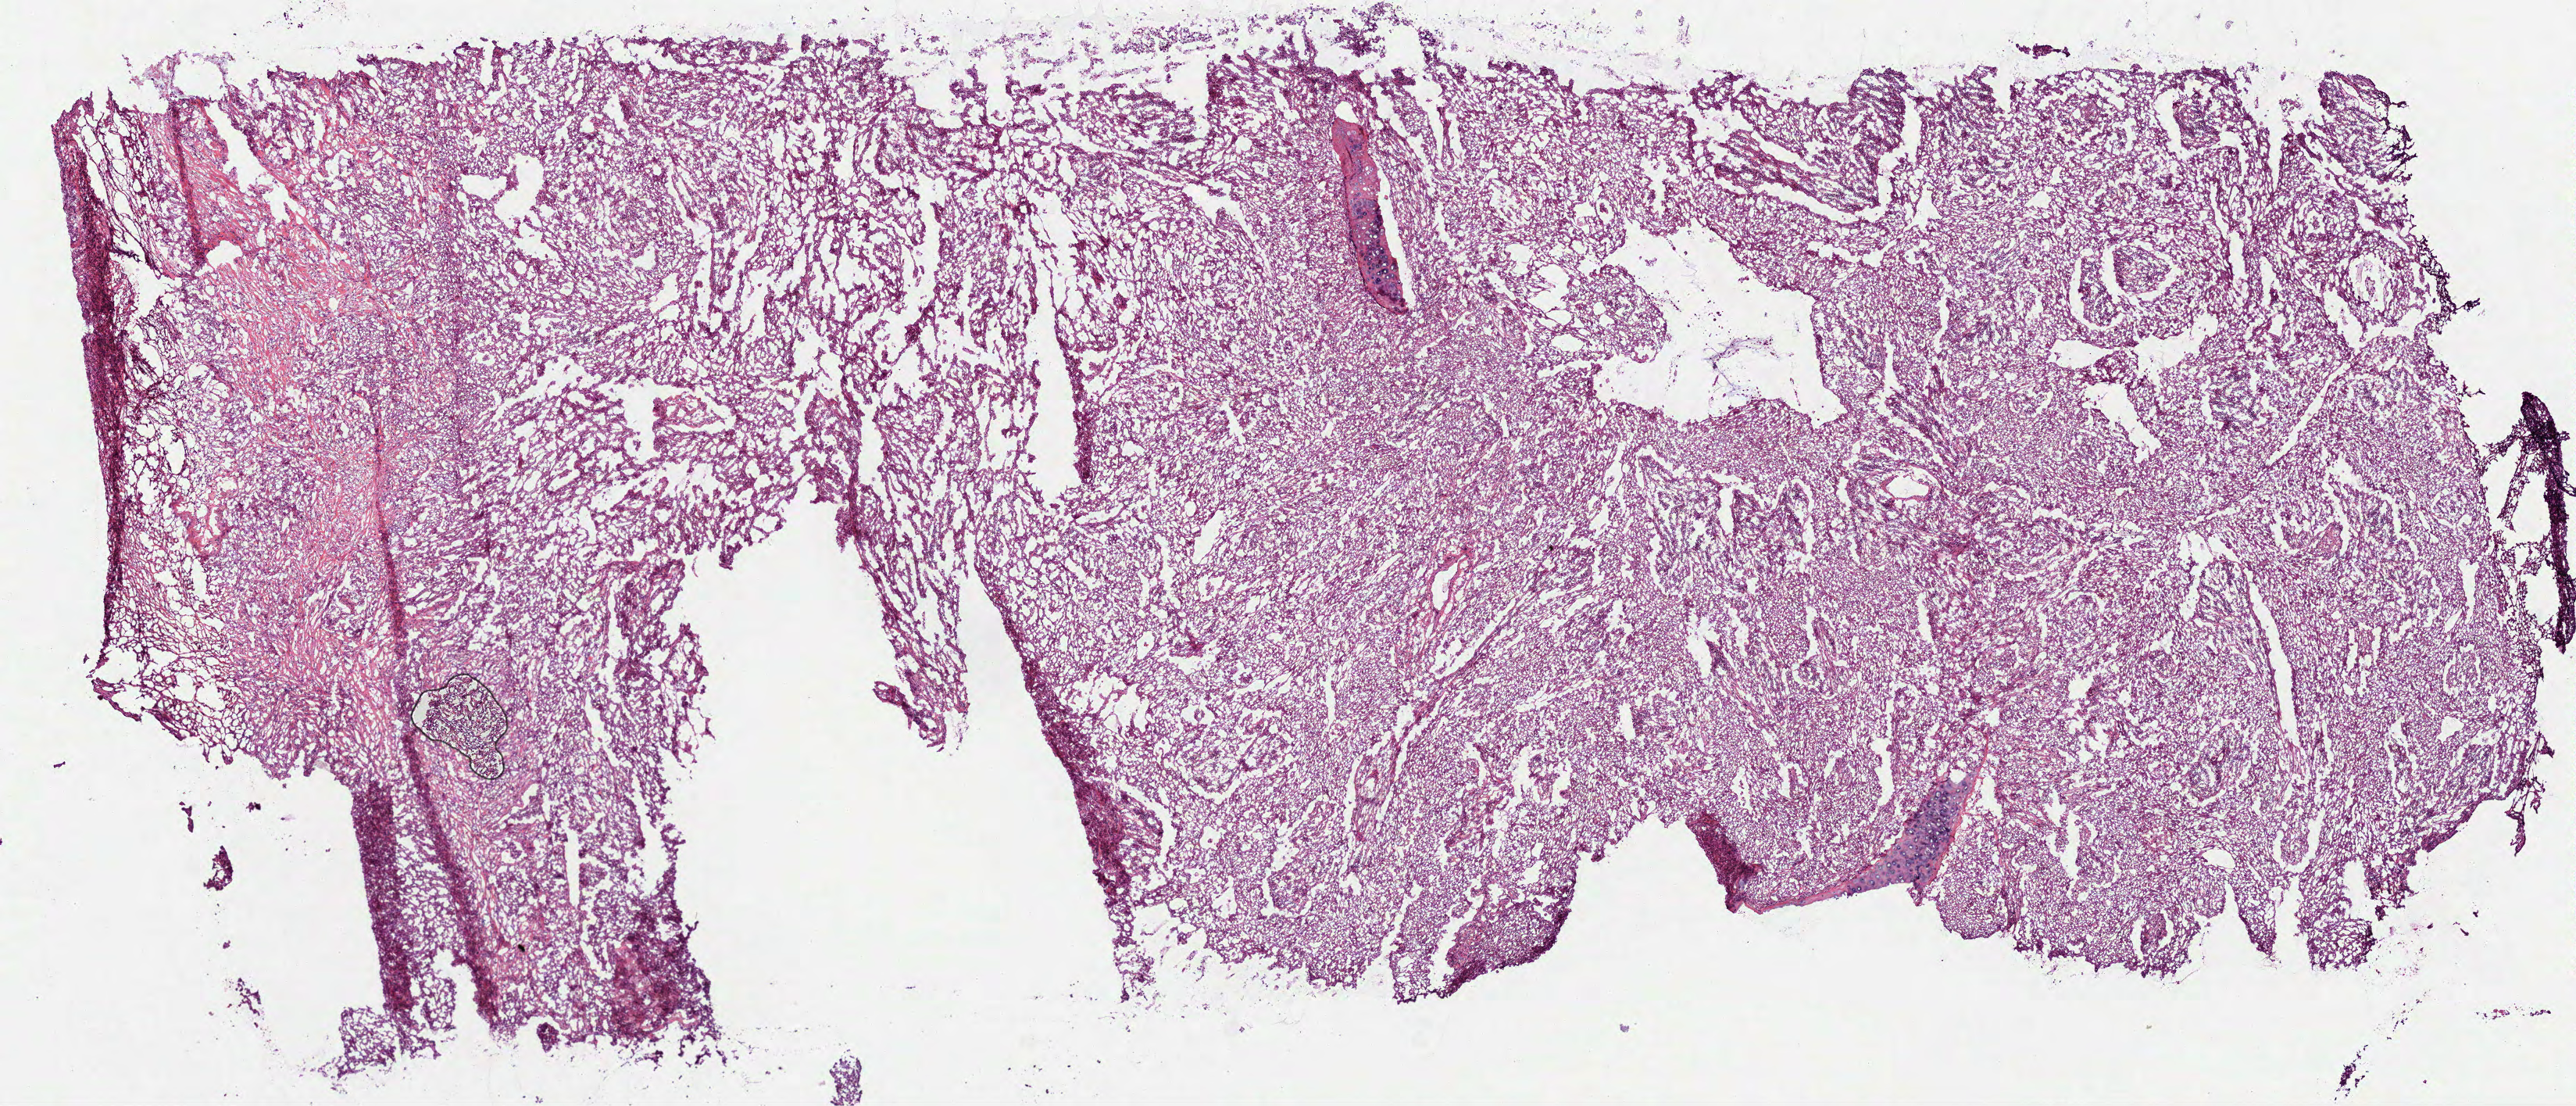
H&E-stained whole-slide image — a low-resolution overview of the entire scanned area, about 13.3 x 5.7 mm; frozen section from the top of the tissue portion; primary tumour sample from the lung. Patient: female, age at initial diagnosis 46 years.
Histologic diagnosis: Adenocarcinoma, NOS (middle lobe, lung).